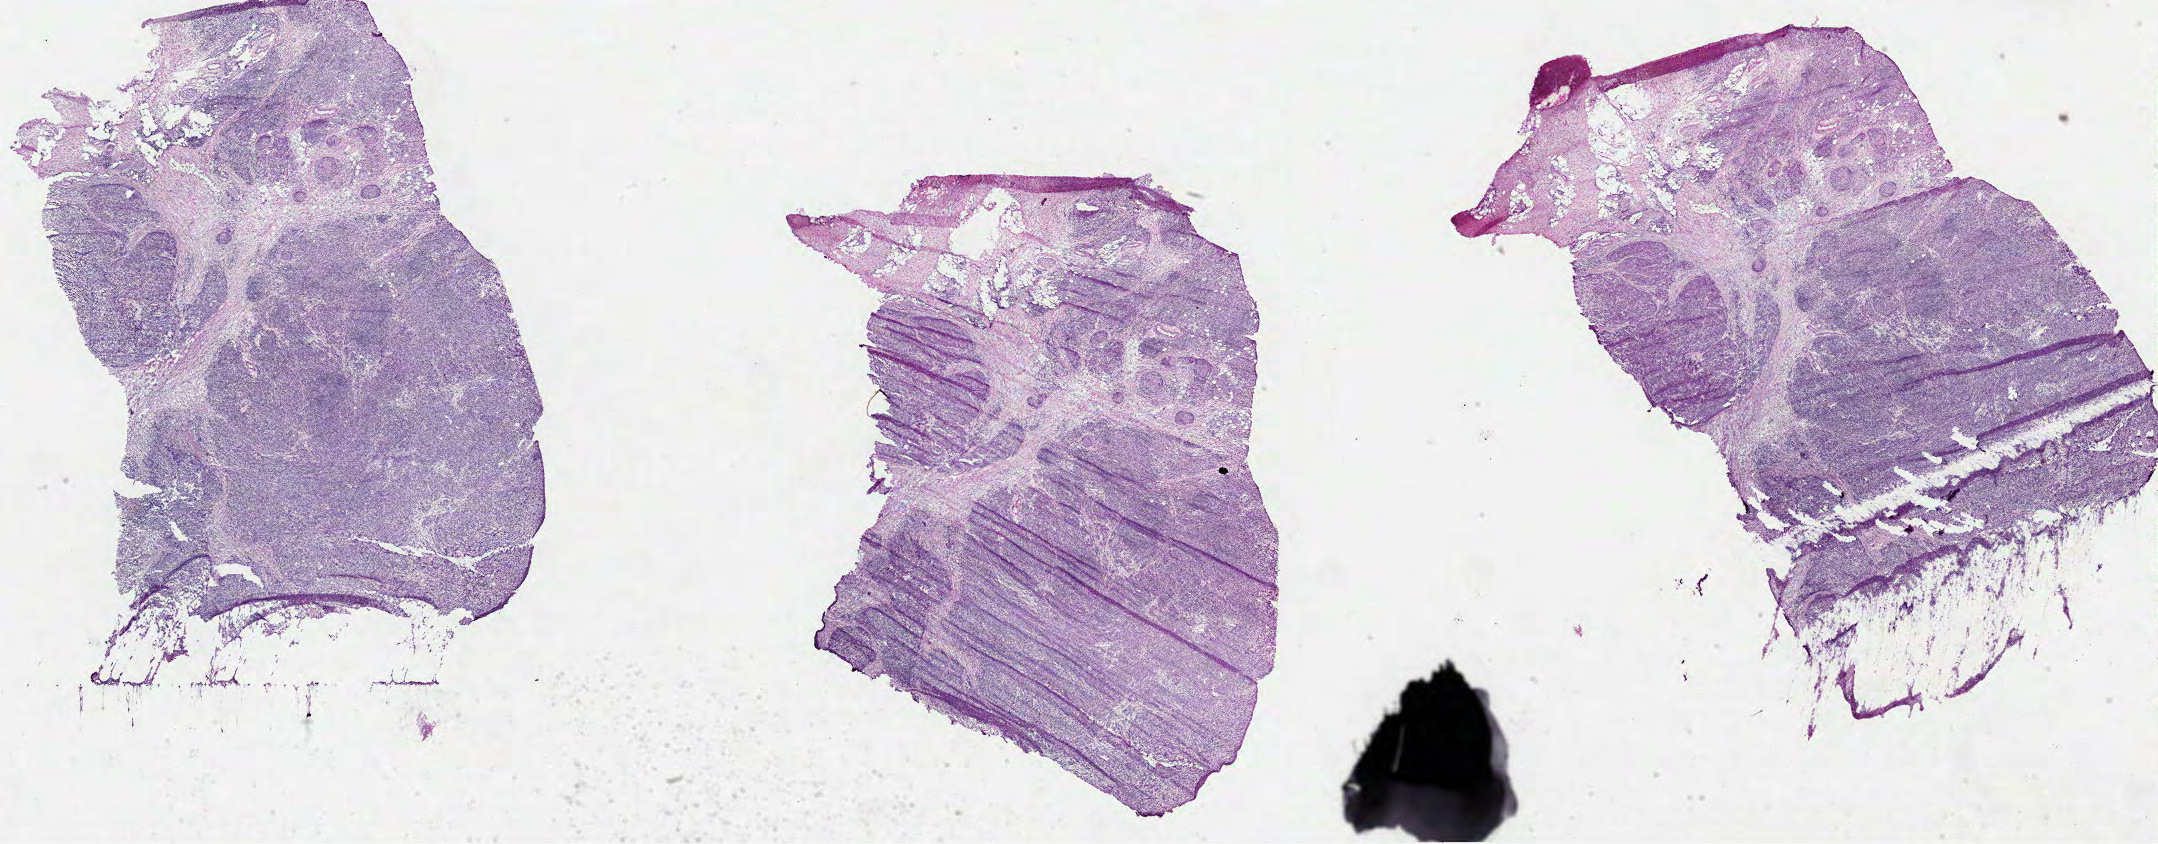
Whole-slide histology image, H&E, shown as a low-resolution overview of the whole scanned area (about 34.8 x 13.6 mm, slide scanned at 40x), formalin-fixed paraffin-embedded (FFPE) diagnostic section, sample: primary tumour, prostate. Patient: male, age at initial diagnosis 72 years. Gleason score: 7 (3+4).
* histologic diagnosis: Acinar cell carcinoma (prostate gland)
* lymph nodes positive (case pathology): 0 of 7 examined